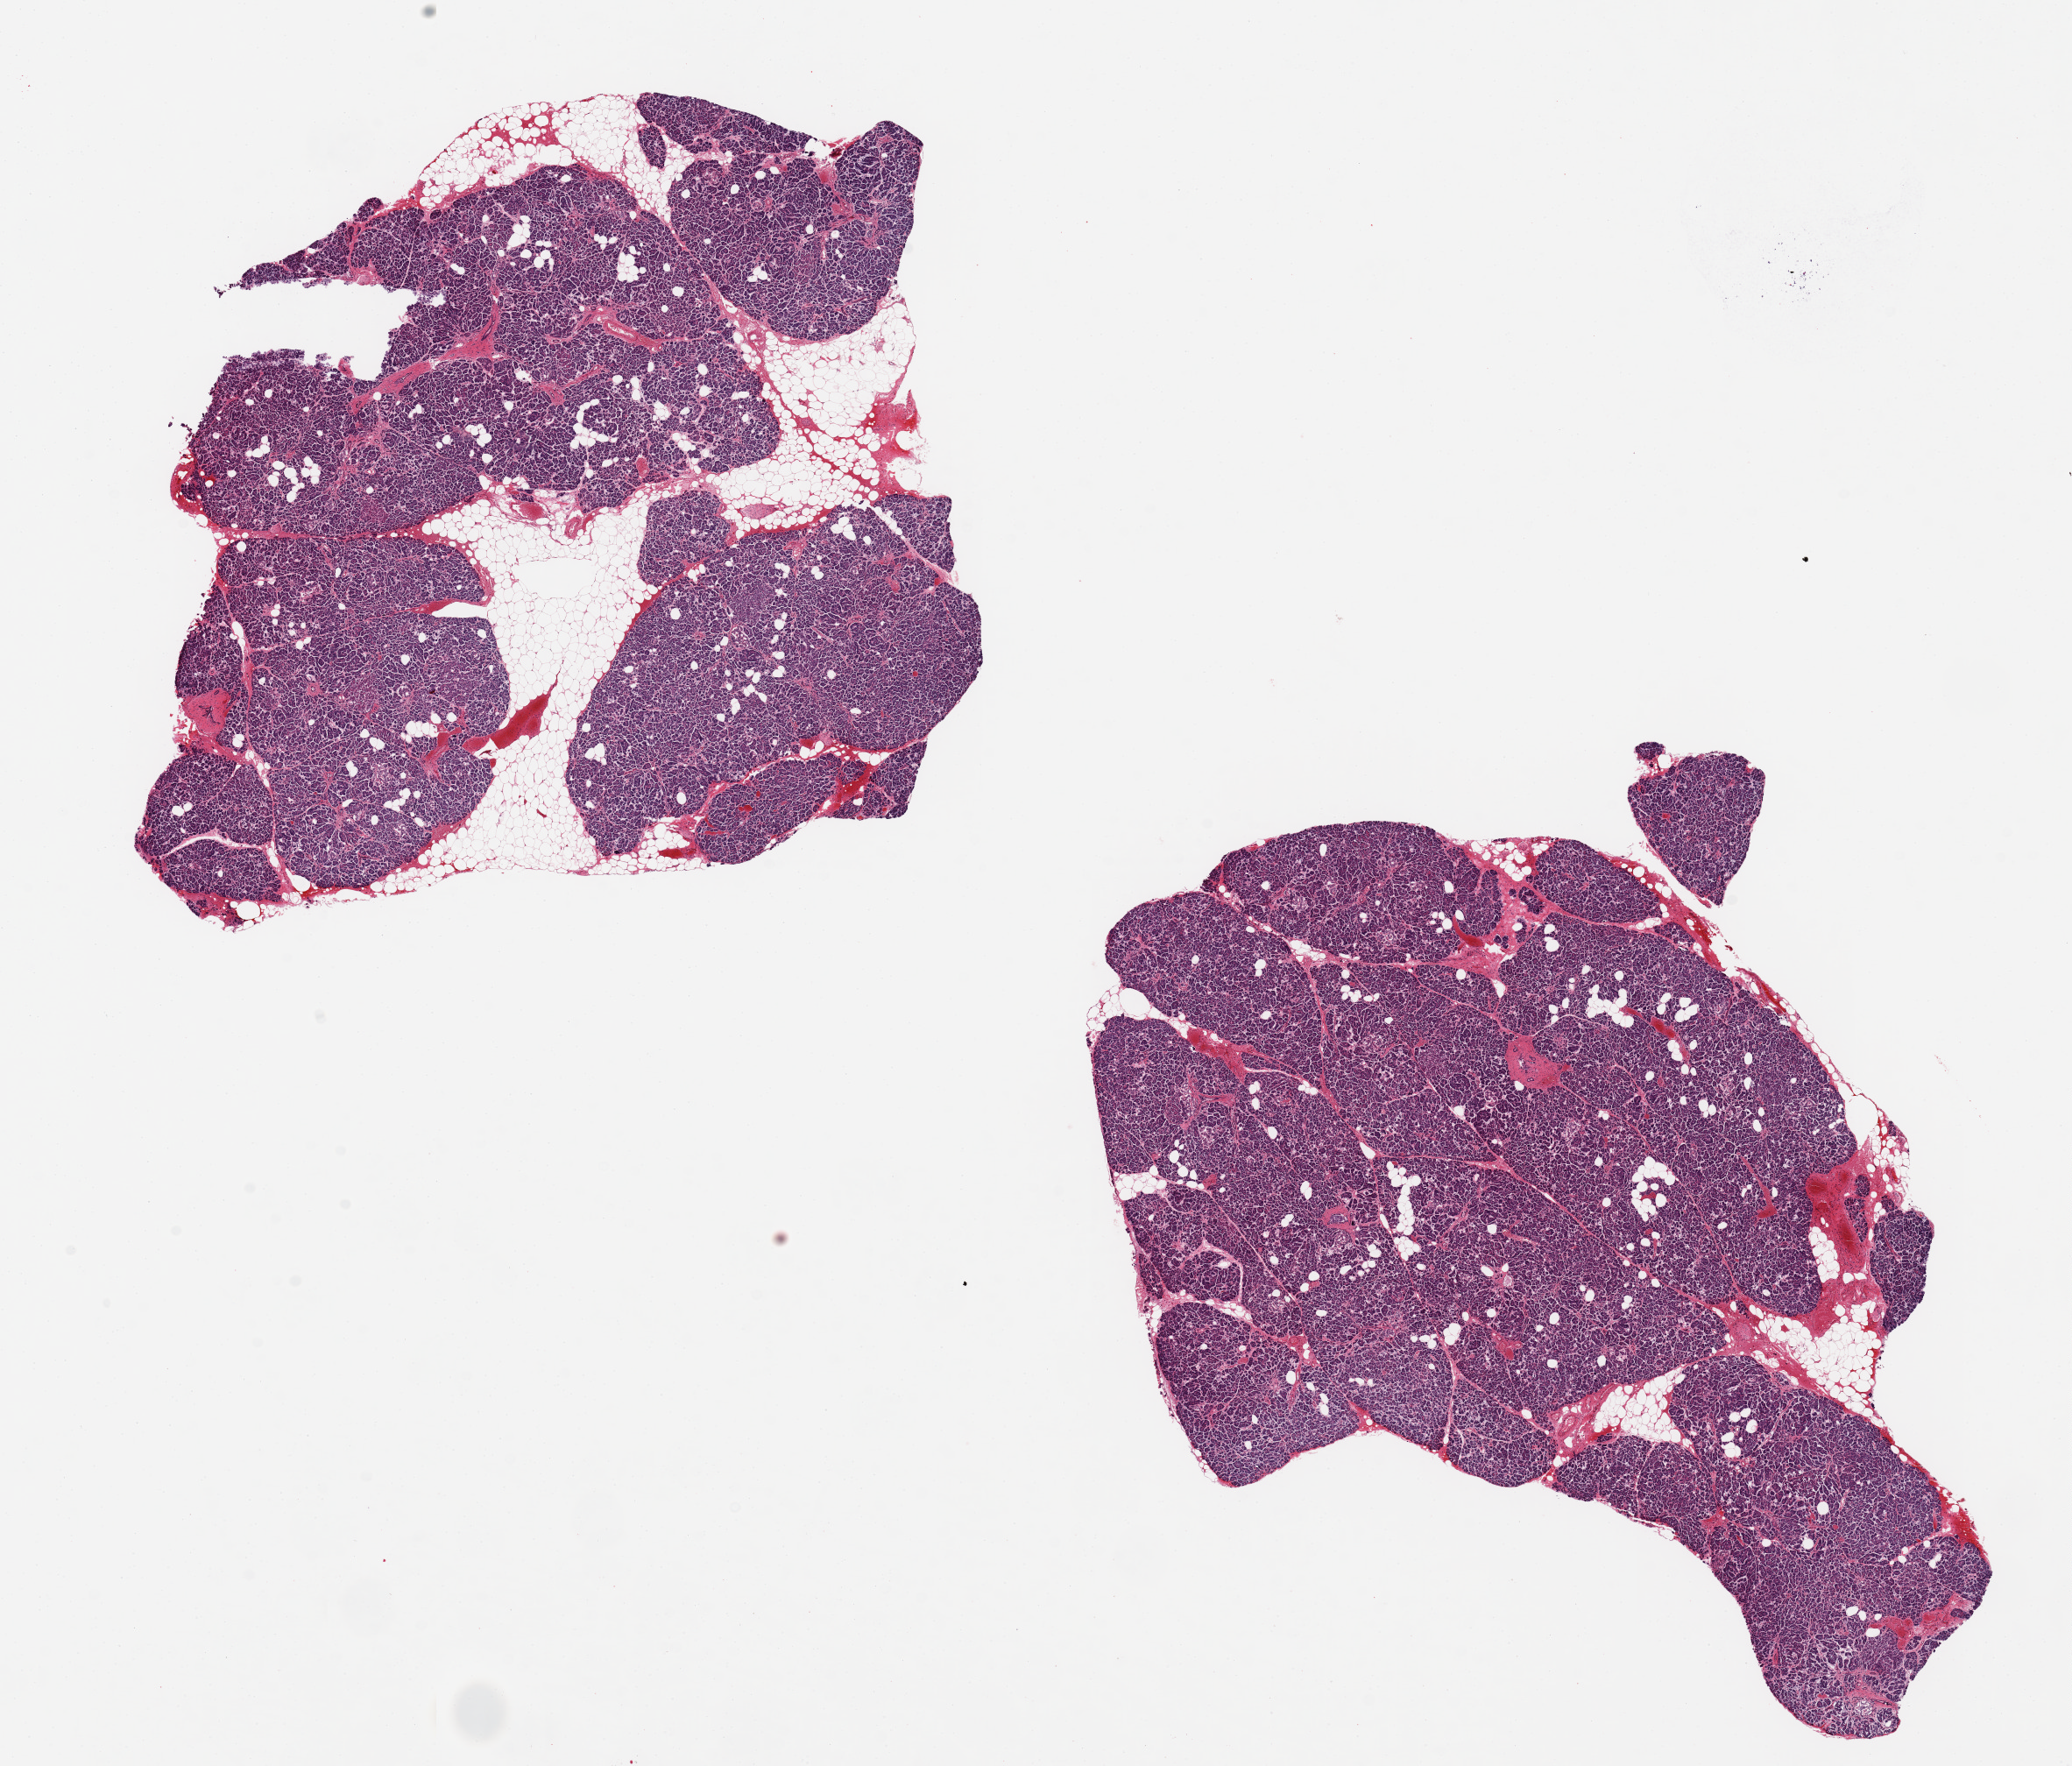
Whole-slide image, hematoxylin and eosin (H&E) stain, shown as a low-resolution overview of the whole scanned area (about 18.7 x 15.9 mm, slide scanned at 20x); PAXgene-fixed paraffin-embedded (PFPE) section; section of pancreas (target tissue); tissue donor sample. Male donor.
• pathologist's review note for this sample: 2 pieces 10x7 & 9x7 mm; ~10-20% adipose within aliquot